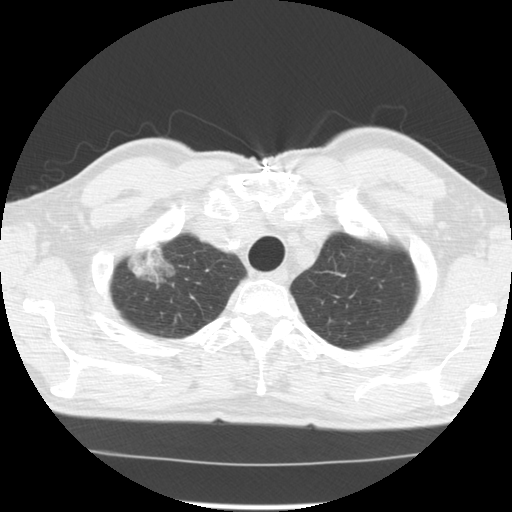
Low-dose screening chest CT, axial slice; third screening round (two years after baseline); lung window (W 1500 / L -600 HU); 2.5 mm slice thickness; standard (soft-tissue) reconstruction kernel (STANDARD); 120 kVp; slice 18 of 128 in the series; 512 × 512 image matrix. Male participant, aged 64 years at enrolment. Former smoker at enrolment.
Expert reader's lesion annotation, bounding box <119,236,188,294> (left, top, right, bottom; pixels). The screening reader recorded 3 non-calcified nodules or masses ≥4 mm on this exam; which of them this box marks is not recorded.